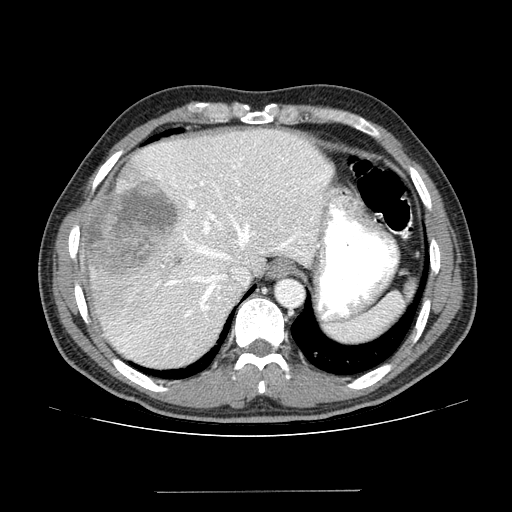
Contrast-enhanced abdominal CT (liver protocol), one axial slice. Reconstruction kernel STANDARD. 100 kVp. One of 2 acquisitions stored at this slice position. Soft-tissue window (W 400 / L 40 HU). 2.5 mm slice thickness. 512 × 512 image matrix, field of view 380 × 380 mm. Case-level facts recorded for this patient, not image findings: diagnosis: hepatocellular carcinoma (patient treated with transarterial chemoembolisation; whether this scan precedes or follows treatment is not stated here); TNM stage (as recorded): Stage-I; Child-Pugh class: A; tumour differentiation: poorly differentiated.
Annotated regions visible in this slice (semi-automatic segmentation, software-assisted and operator-edited):
- abdominal aorta: box from (x=278, y=282) to (x=303, y=306) px
- liver parenchyma outside the tumour (the mass and vessels are separate outlines, so this box may not span the whole liver): (x=78, y=130)–(x=332, y=368)
- mass: (x=81, y=178)–(x=177, y=291)
- liver vessels: (x=116, y=135)–(x=328, y=352)